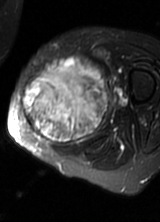
MRI of an extremity soft-tissue mass, one axial slice. Slice 27 of 69 in the series (ordered by position). T2-weighted fat-saturated. MR volume resampled by the dataset authors to the PET/CT grid (not the native acquisition matrix). 3.27 mm slice thickness. 160 × 222 image matrix, field of view 156 × 217 mm. Female patient. From the clinical record (not read from this slice): histological type: pleomorphic leiomyosarcoma; grade: high; site of the primary tumour: left thigh.
Structures marked on this image (expert contour drawn on MRI and transferred to this co-registered scan by the dataset authors):
- gross tumour volume including surrounding oedema: box from (x=22, y=57) to (x=110, y=146) px
- gross tumour volume (mass): (x=22, y=59)–(x=108, y=146)